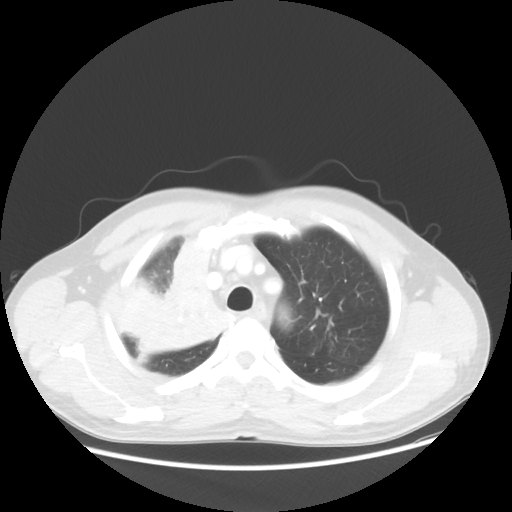
Chest CT, one axial slice. Position 43 of 56 along the scan axis. 100 kVp. Lung window (W 1500 / L -600 HU). 5 mm slice thickness. 512 × 512 image matrix, field of view 398 × 398 mm. Male patient, age 60 years. From the clinical record (not read from this slice): clinical TNM (as recorded): T2a N1 M0.
Annotated regions visible in this slice (rectangle marked by the reading radiologist):
- lung tumour (recorded histology: squamous cell carcinoma): bounding box [x1, y1, x2, y2] px = [128, 228, 232, 362]